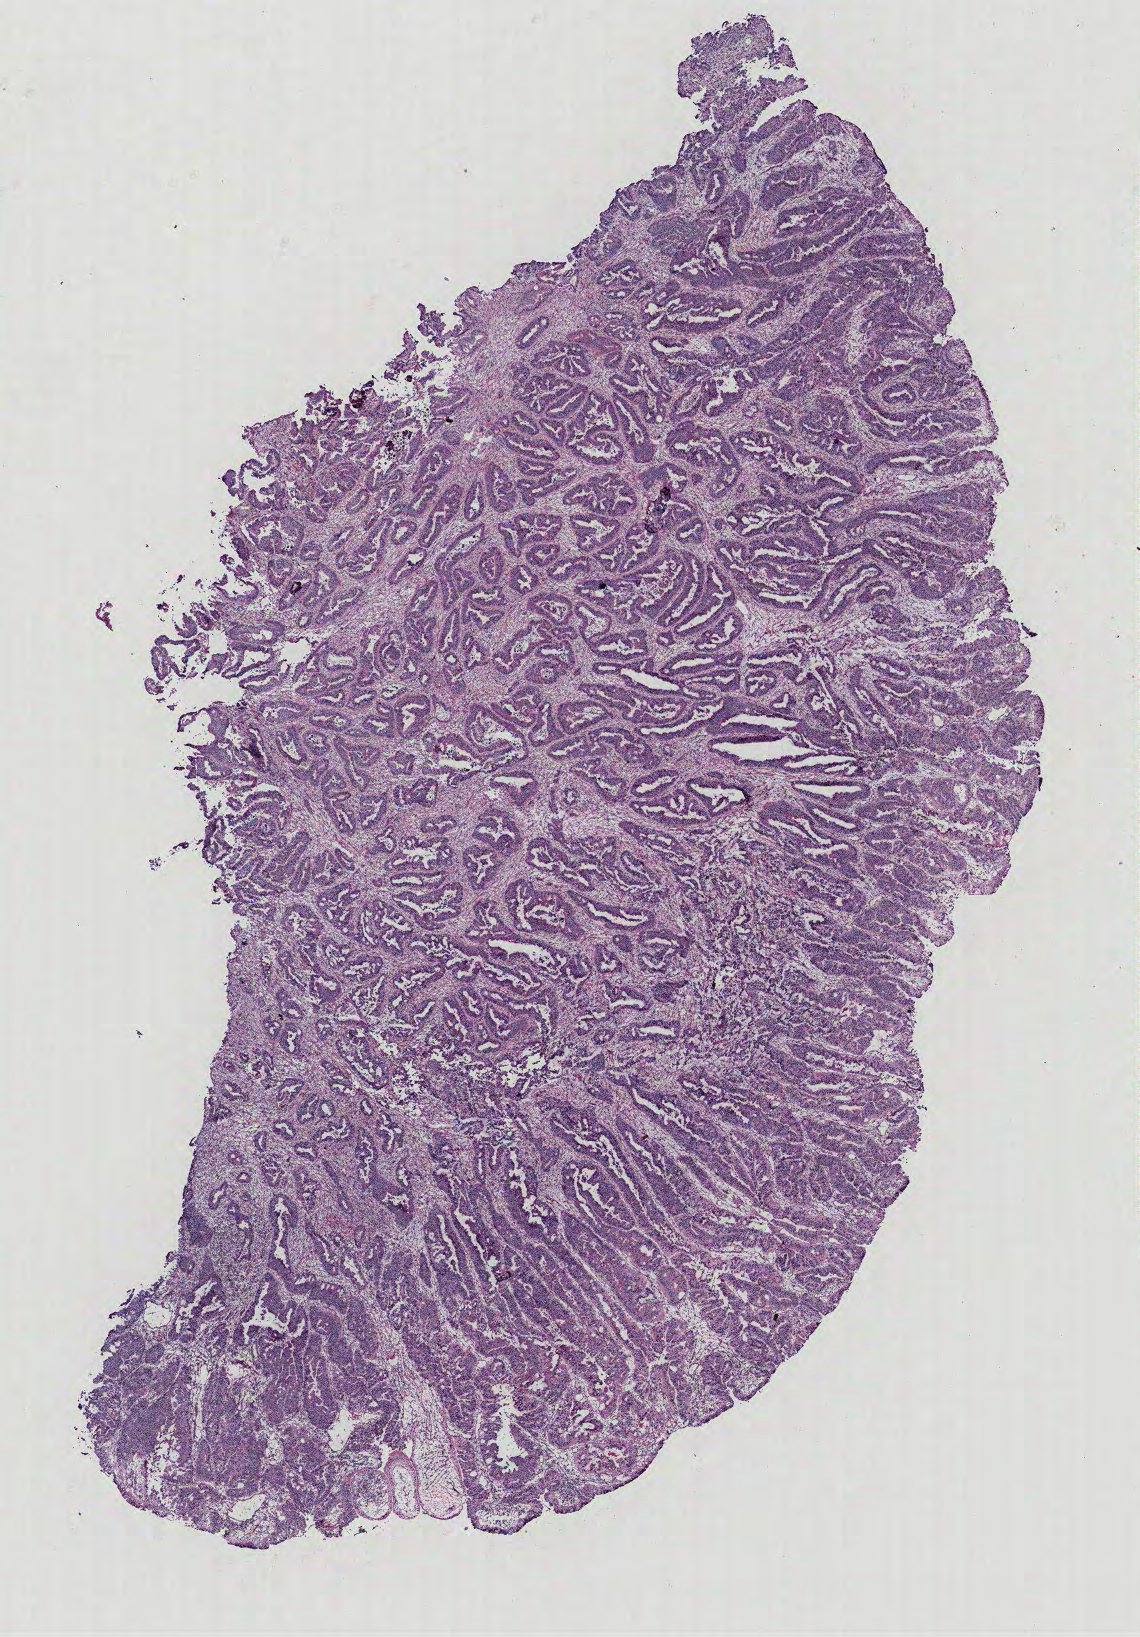
Digitized H&E tissue section (whole slide) — low-resolution overview of the scanned area, about 9.1 x 13.1 mm (from a 40x scan), tumour tissue sample, colon. 55-year-old male patient.
Histologic diagnosis: Adenocarcinoma, NOS. Primary tumour site (as recorded): colon. AJCC pathologic stage: IIIC.